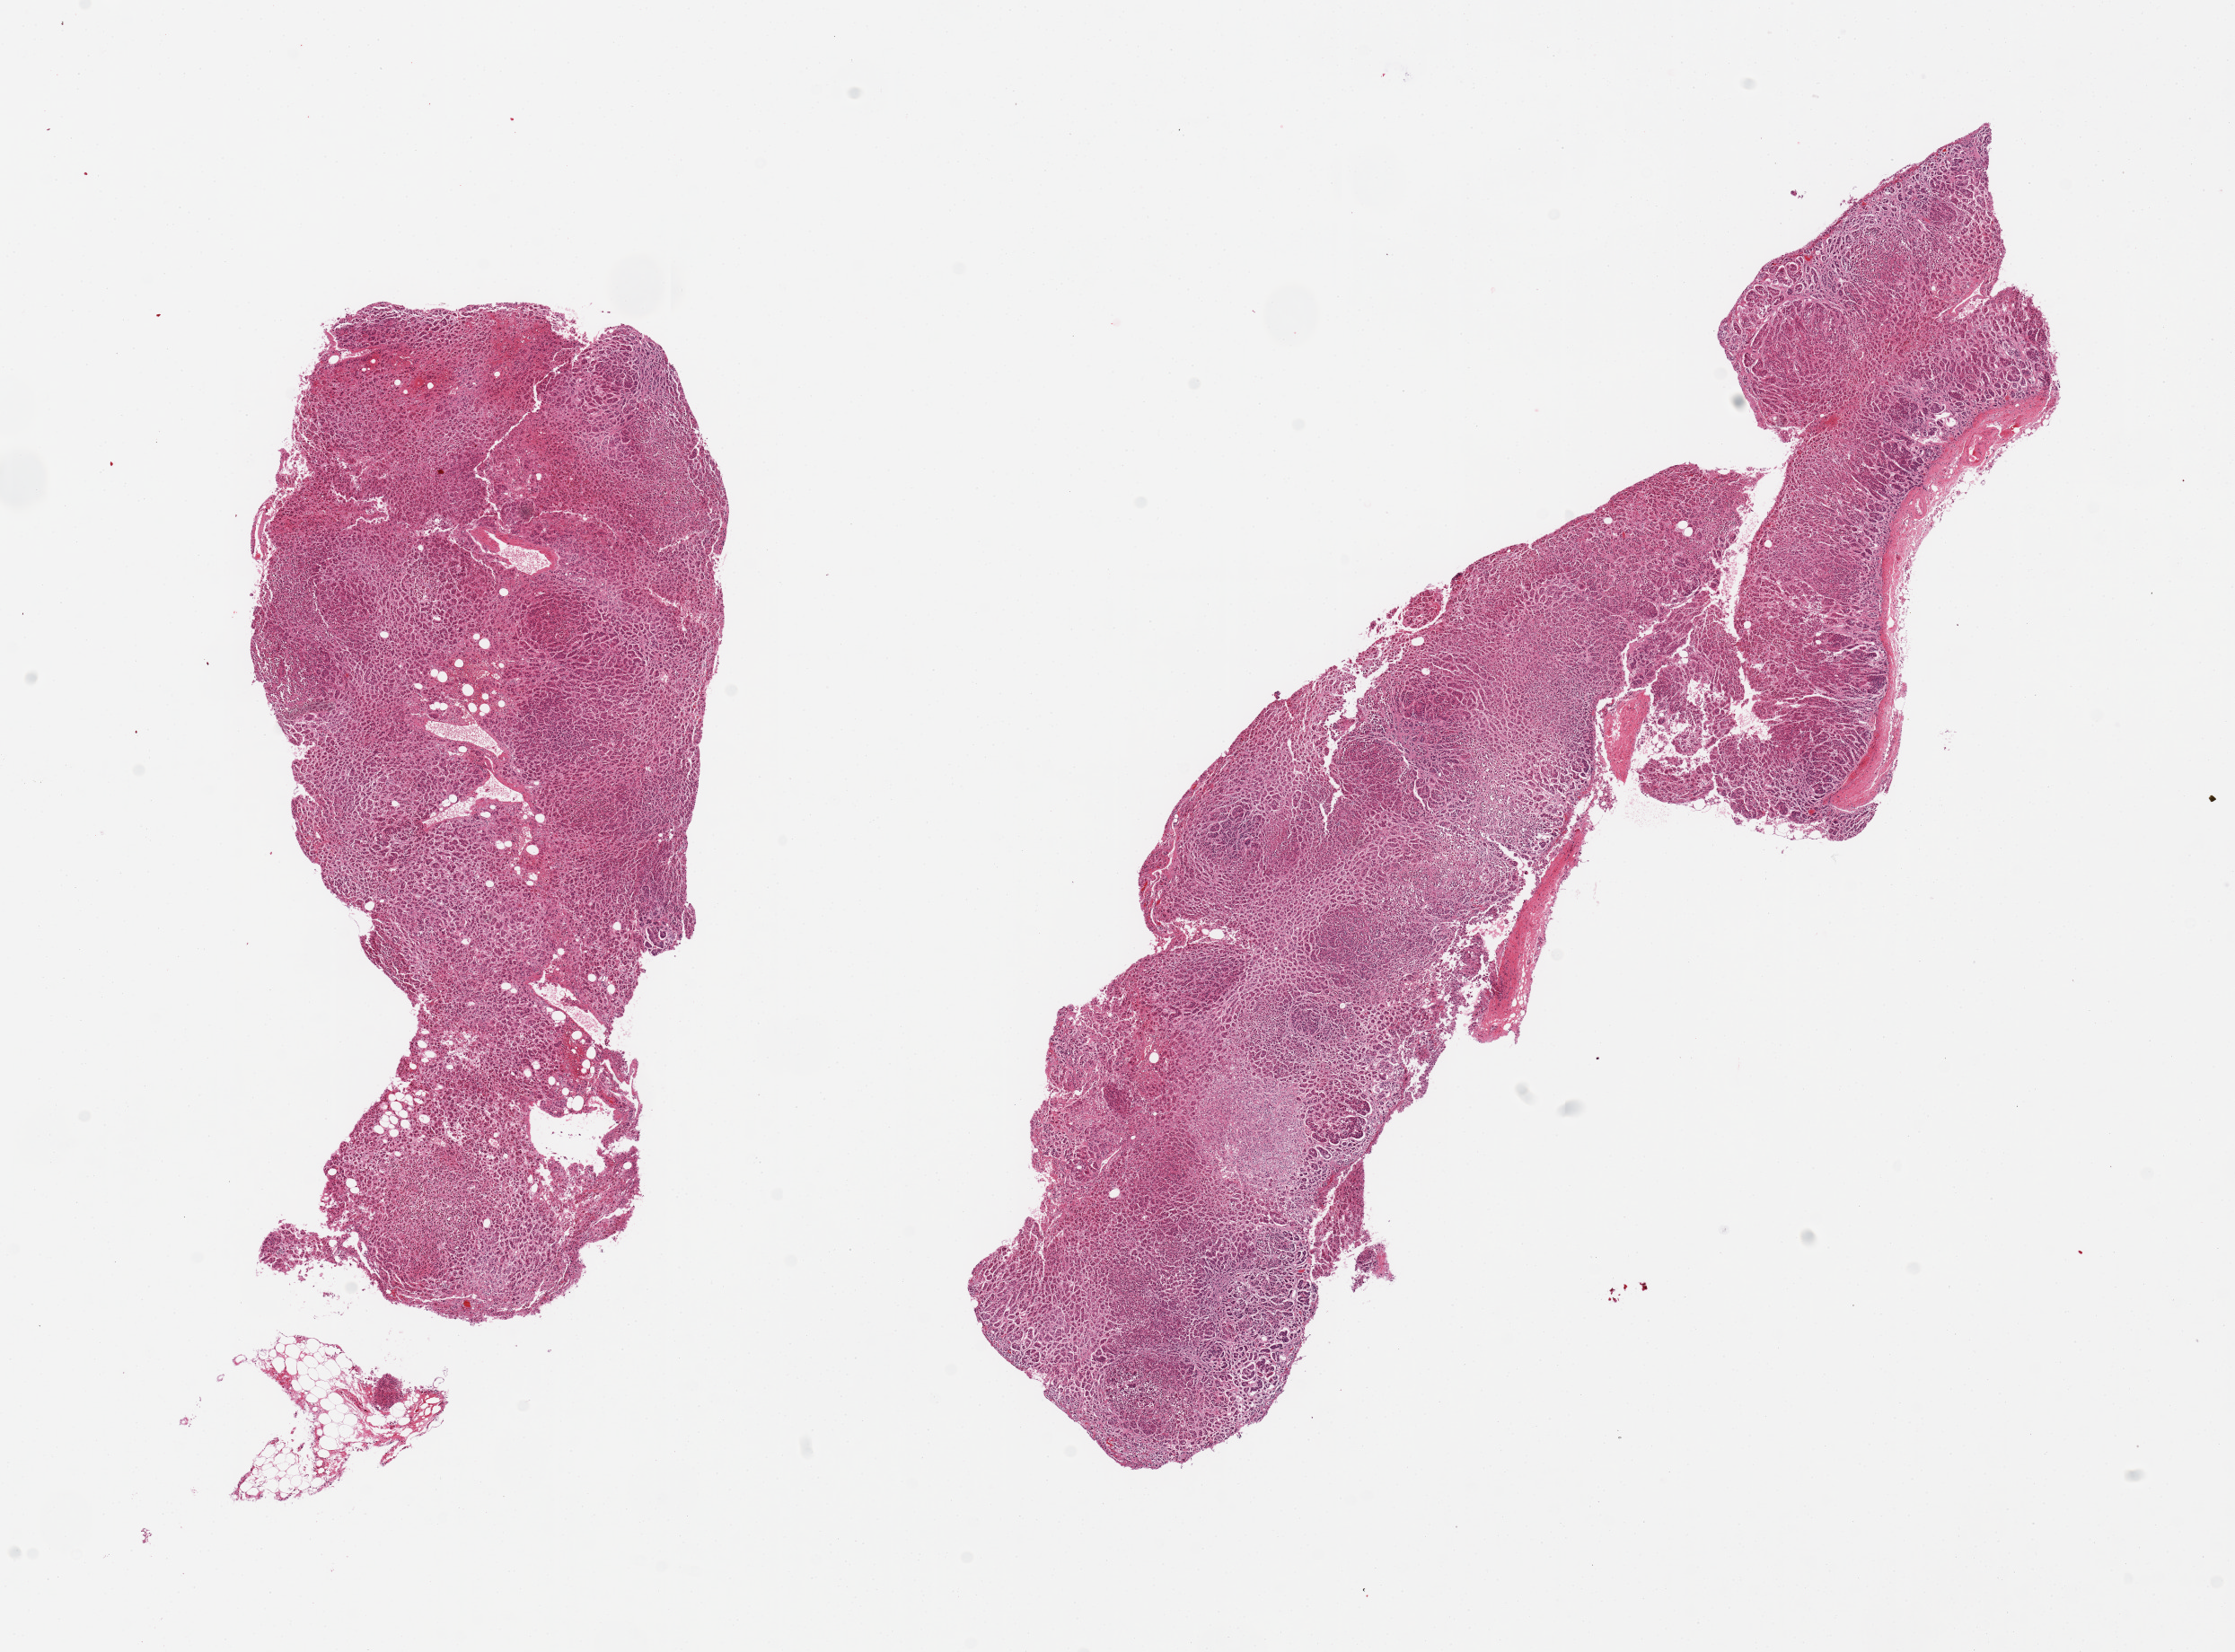
H&E whole-slide image — shown as a low-resolution overview of the whole scanned area (about 19.7 x 14.6 mm). PAXgene-fixed, paraffin-embedded tissue. Sampled site (target tissue): adrenal gland. Tissue donor sample. Male donor.
Reviewer comment on this tissue sample: 2 pieces, all cortex, markedly autolyzed.